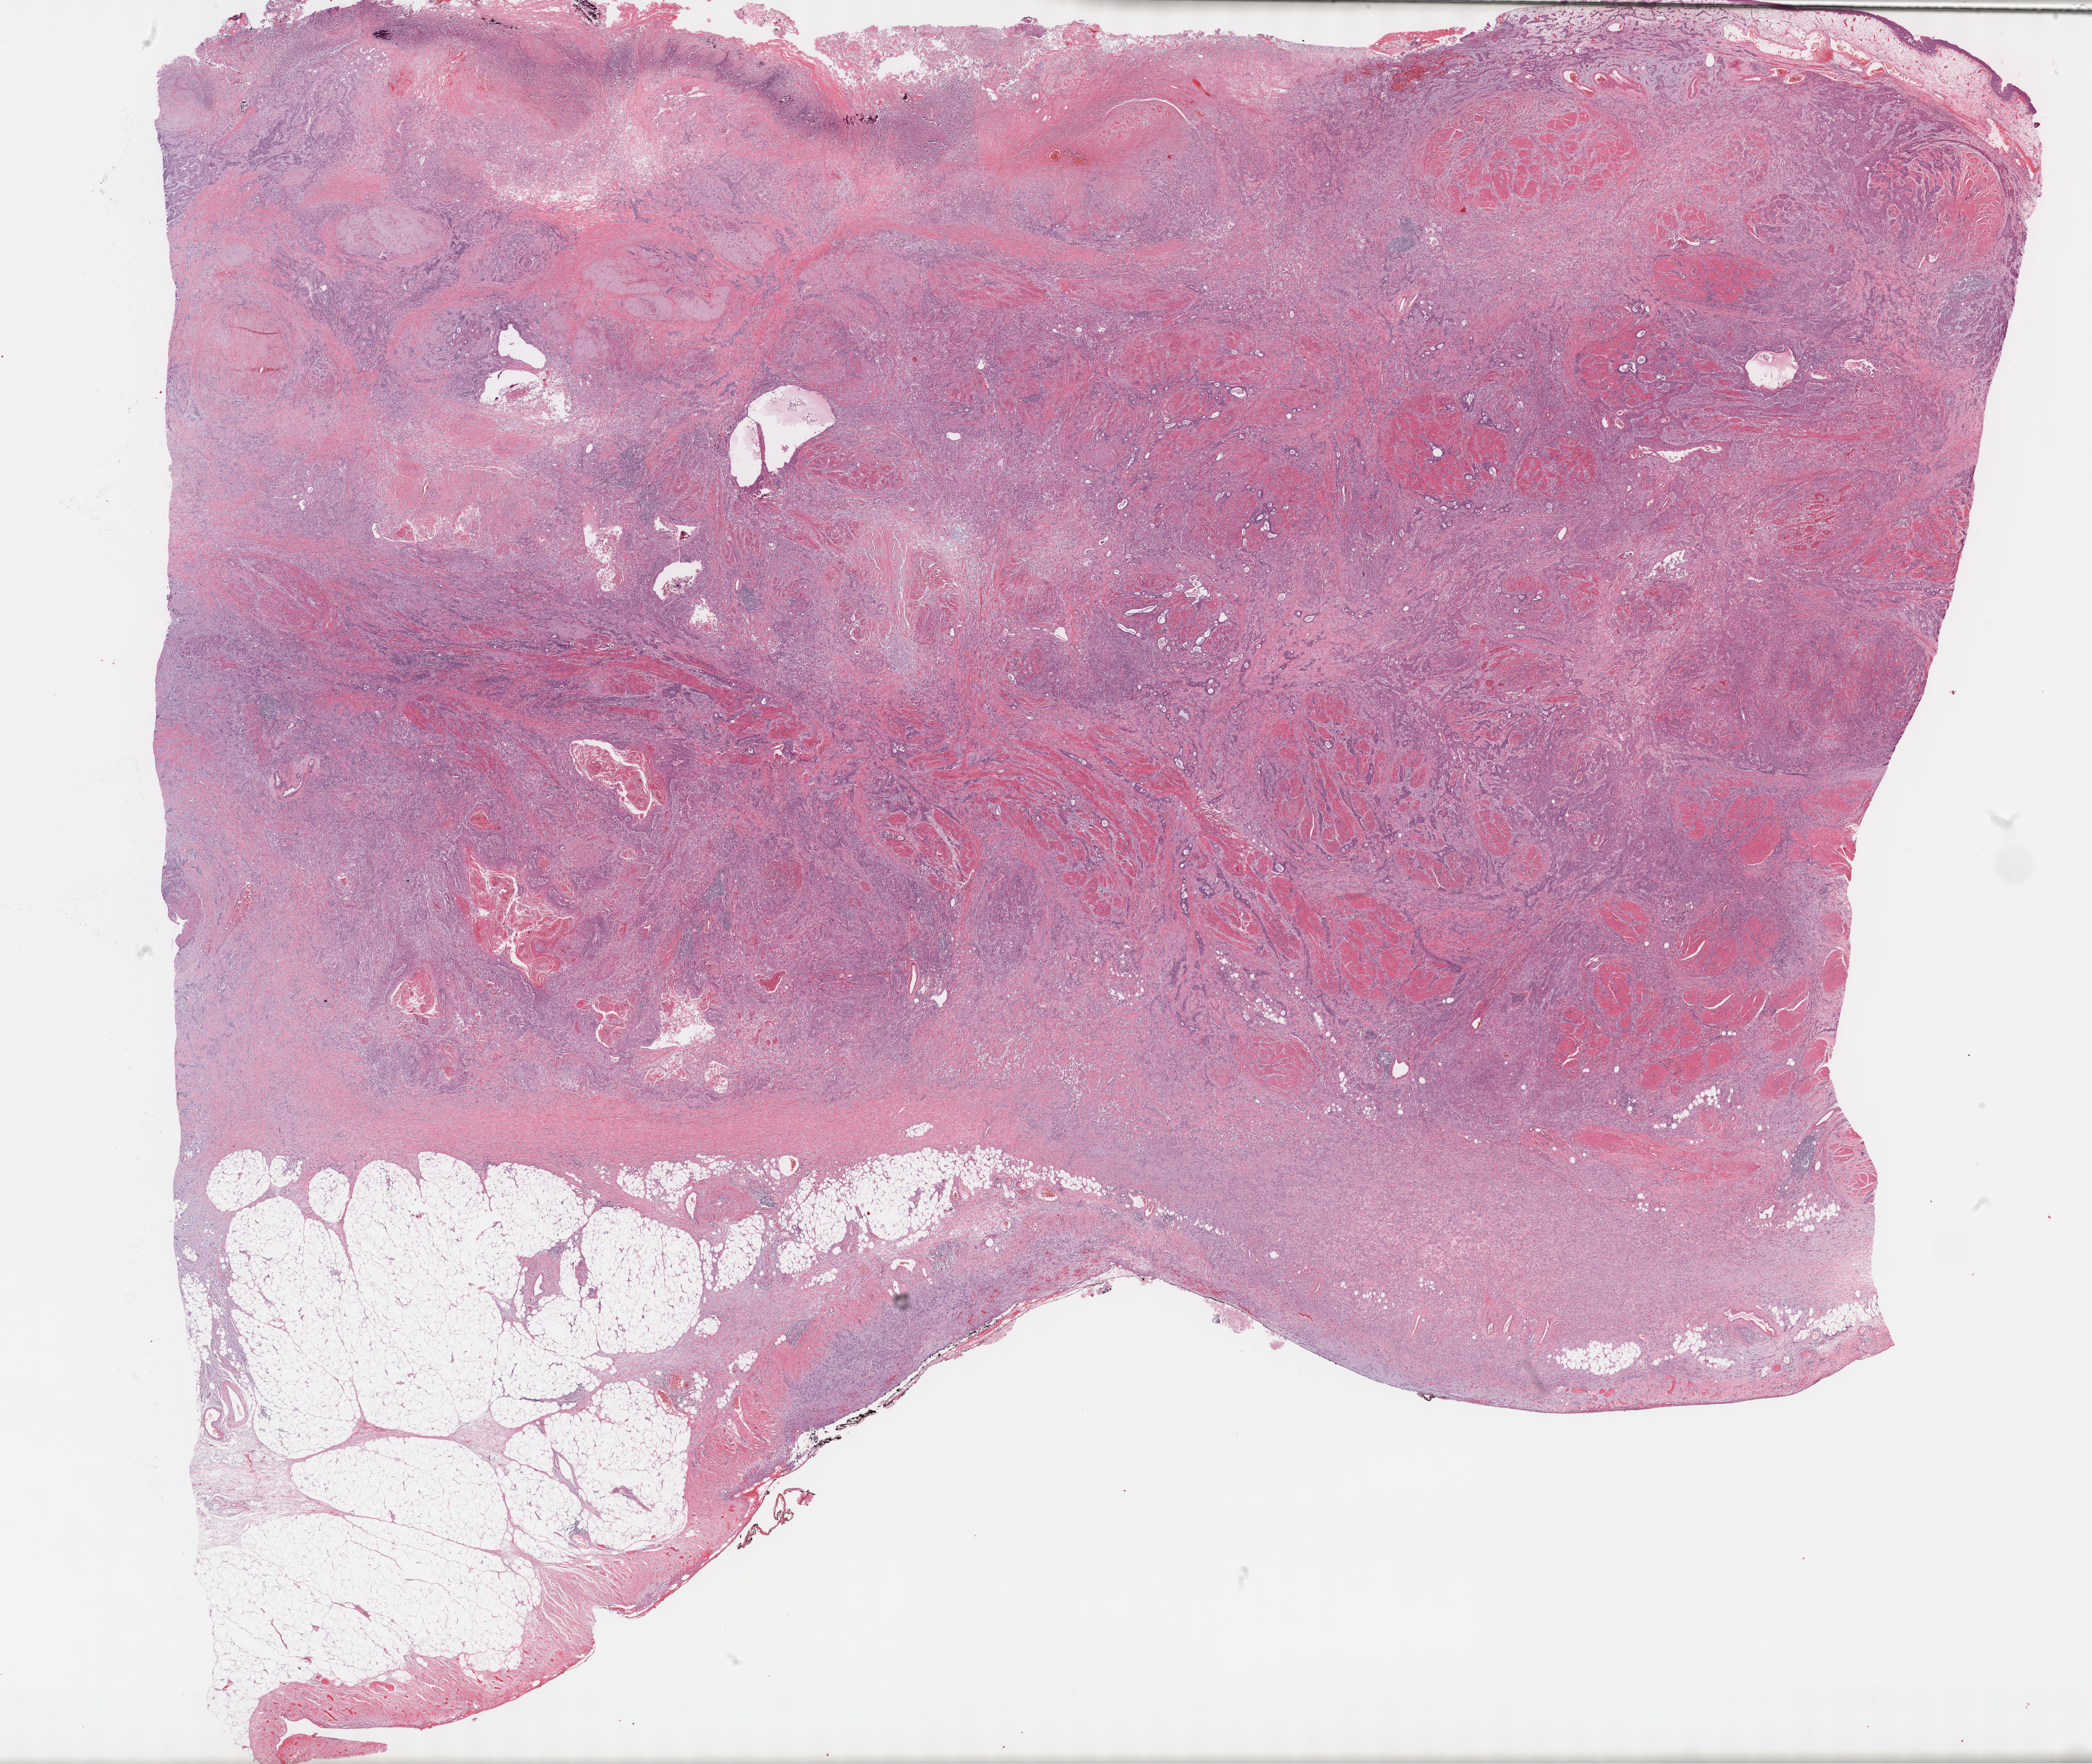
Whole-slide histology image, H&E, low-resolution overview of the scanned area, about 27.7 x 23.3 mm (slide scanned at 40x). Formalin-fixed paraffin-embedded (FFPE) diagnostic section. Sample: primary tumour, bladder. Female, age 75 years at initial diagnosis. Histologic grade: high grade.
Diagnosis: Transitional cell carcinoma. AJCC pathologic stage: IV (5th edition). Lymph nodes positive (case pathology): 5 of 74 examined.